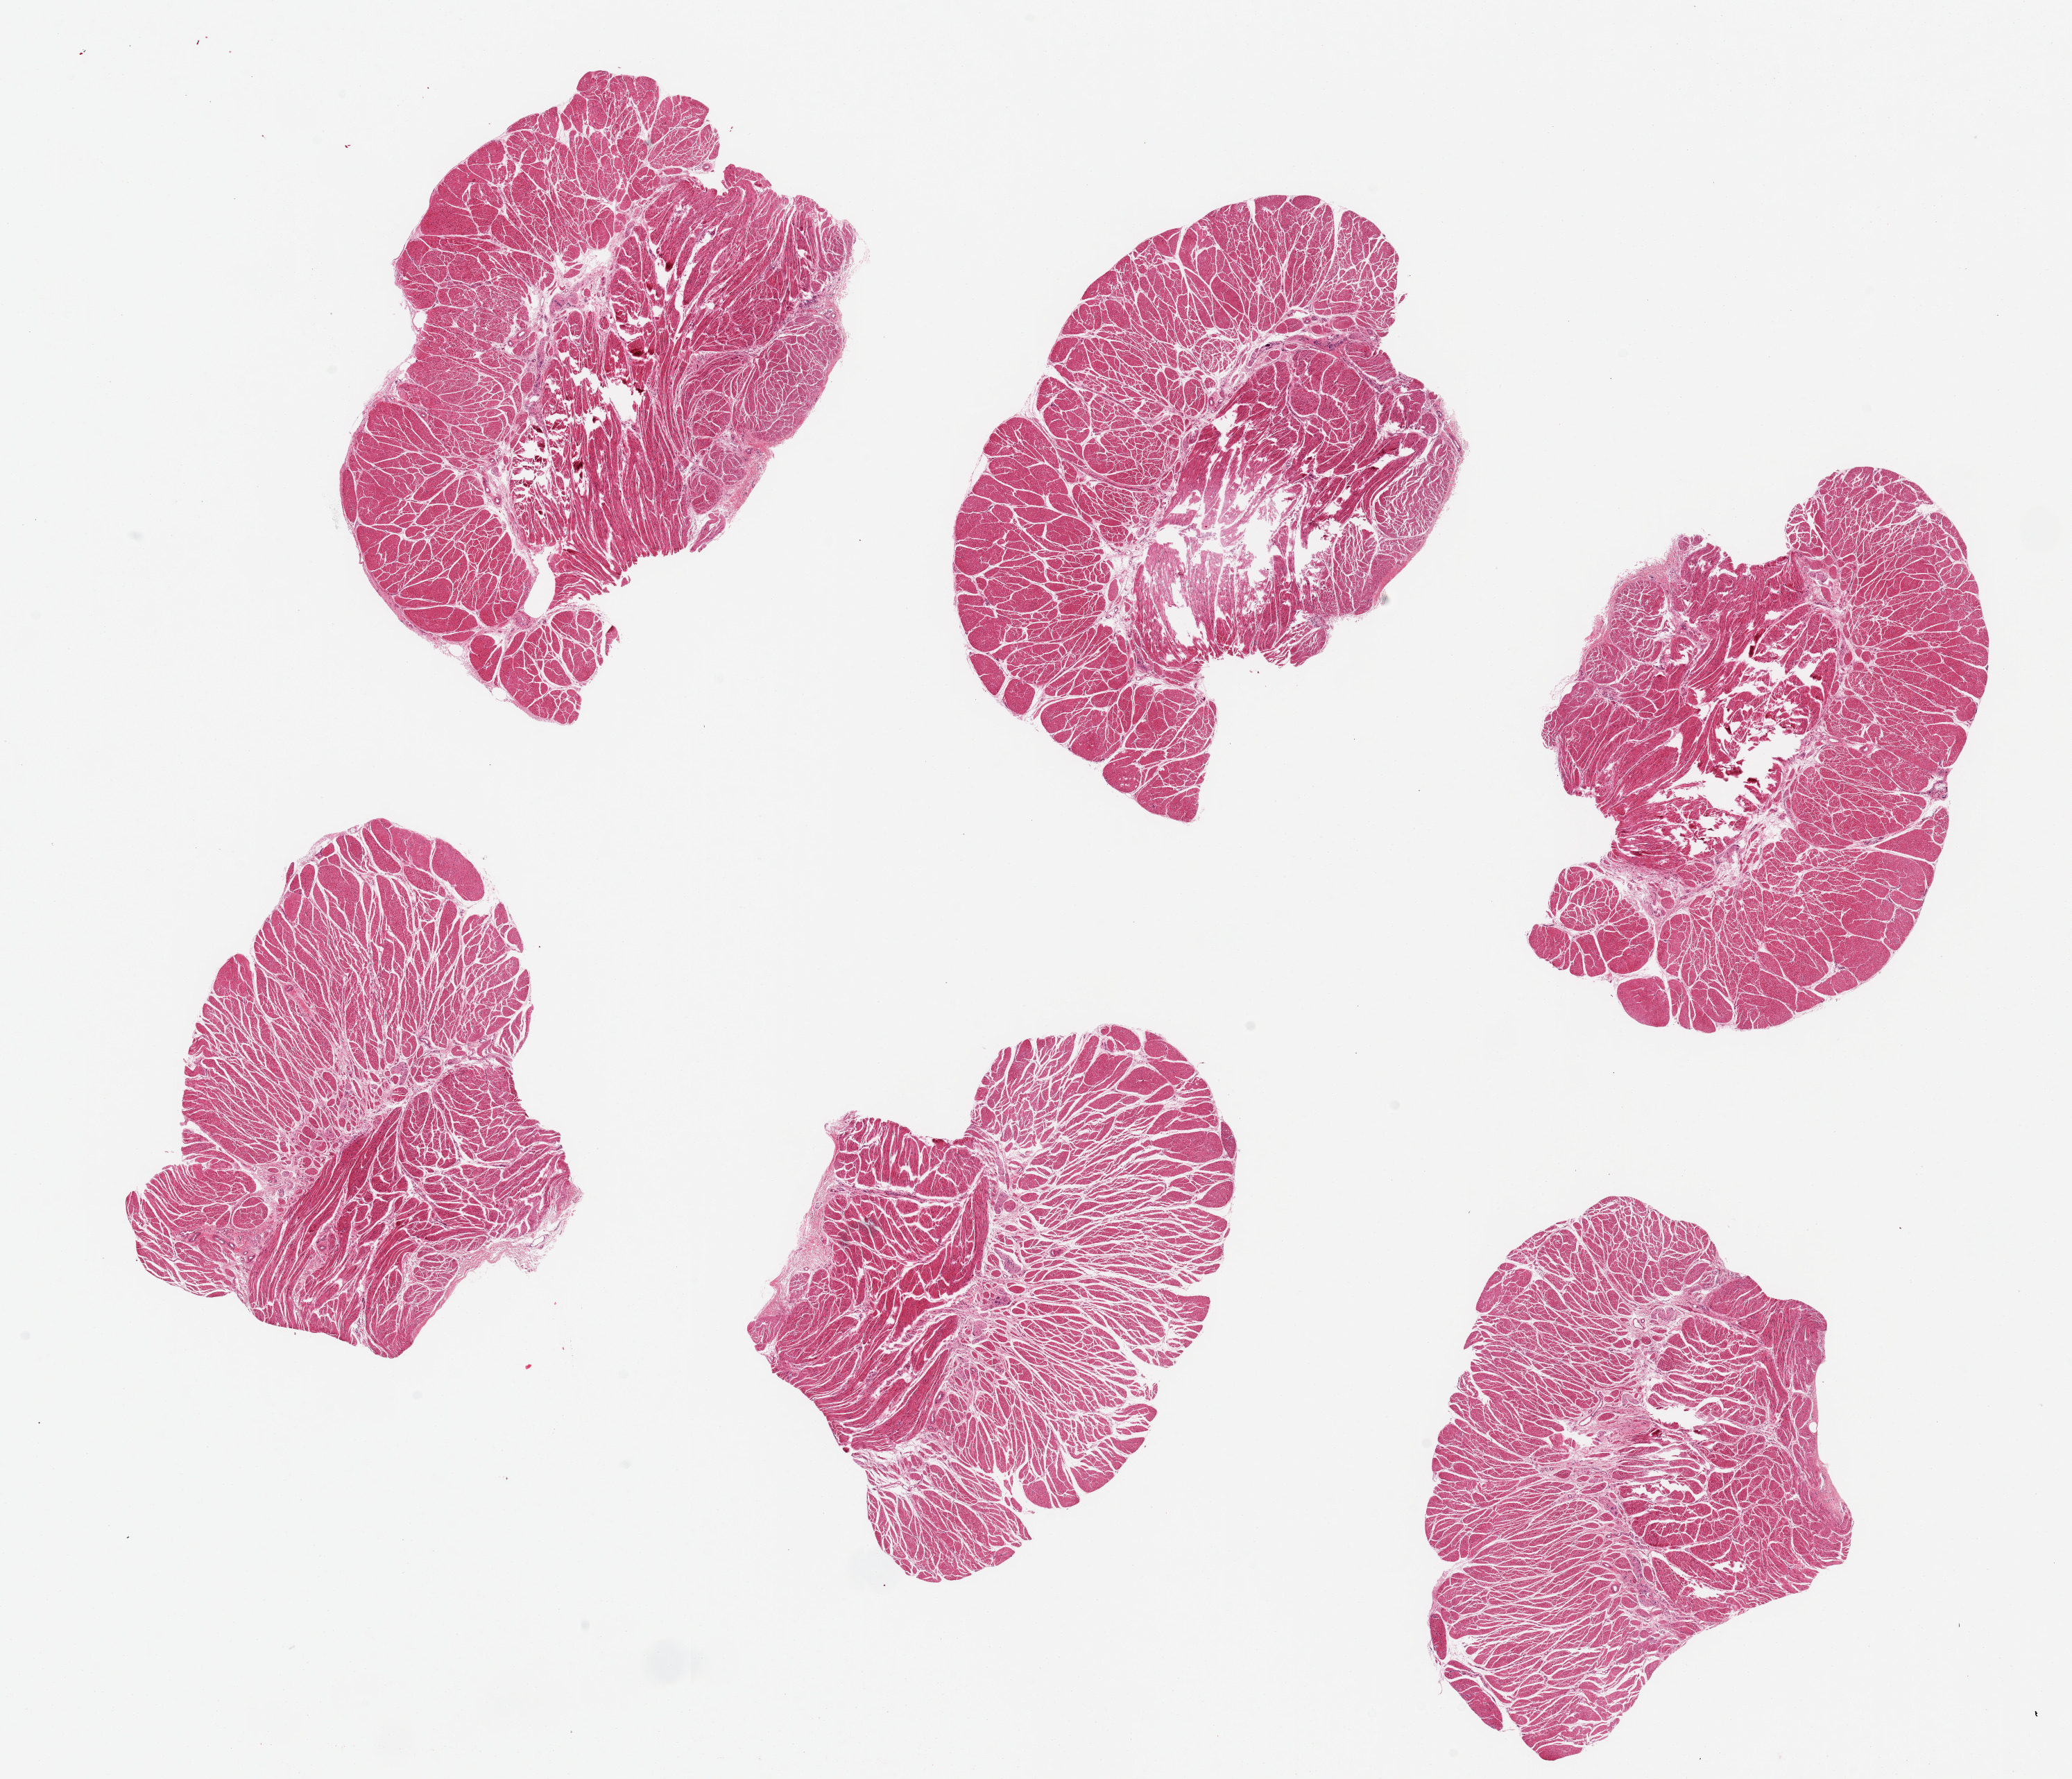
Whole-slide image, hematoxylin and eosin (H&E) stain, brightfield — shown as a low-resolution overview of the whole scanned area (about 23.6 x 20.3 mm), PAXgene-fixed paraffin-embedded (PFPE) section, sampled site (target tissue): esophageal muscle, donor tissue sample. Female donor.
Review note (as recorded): 6 pieces, up to 7x5mm; all muscularis; good specimens.